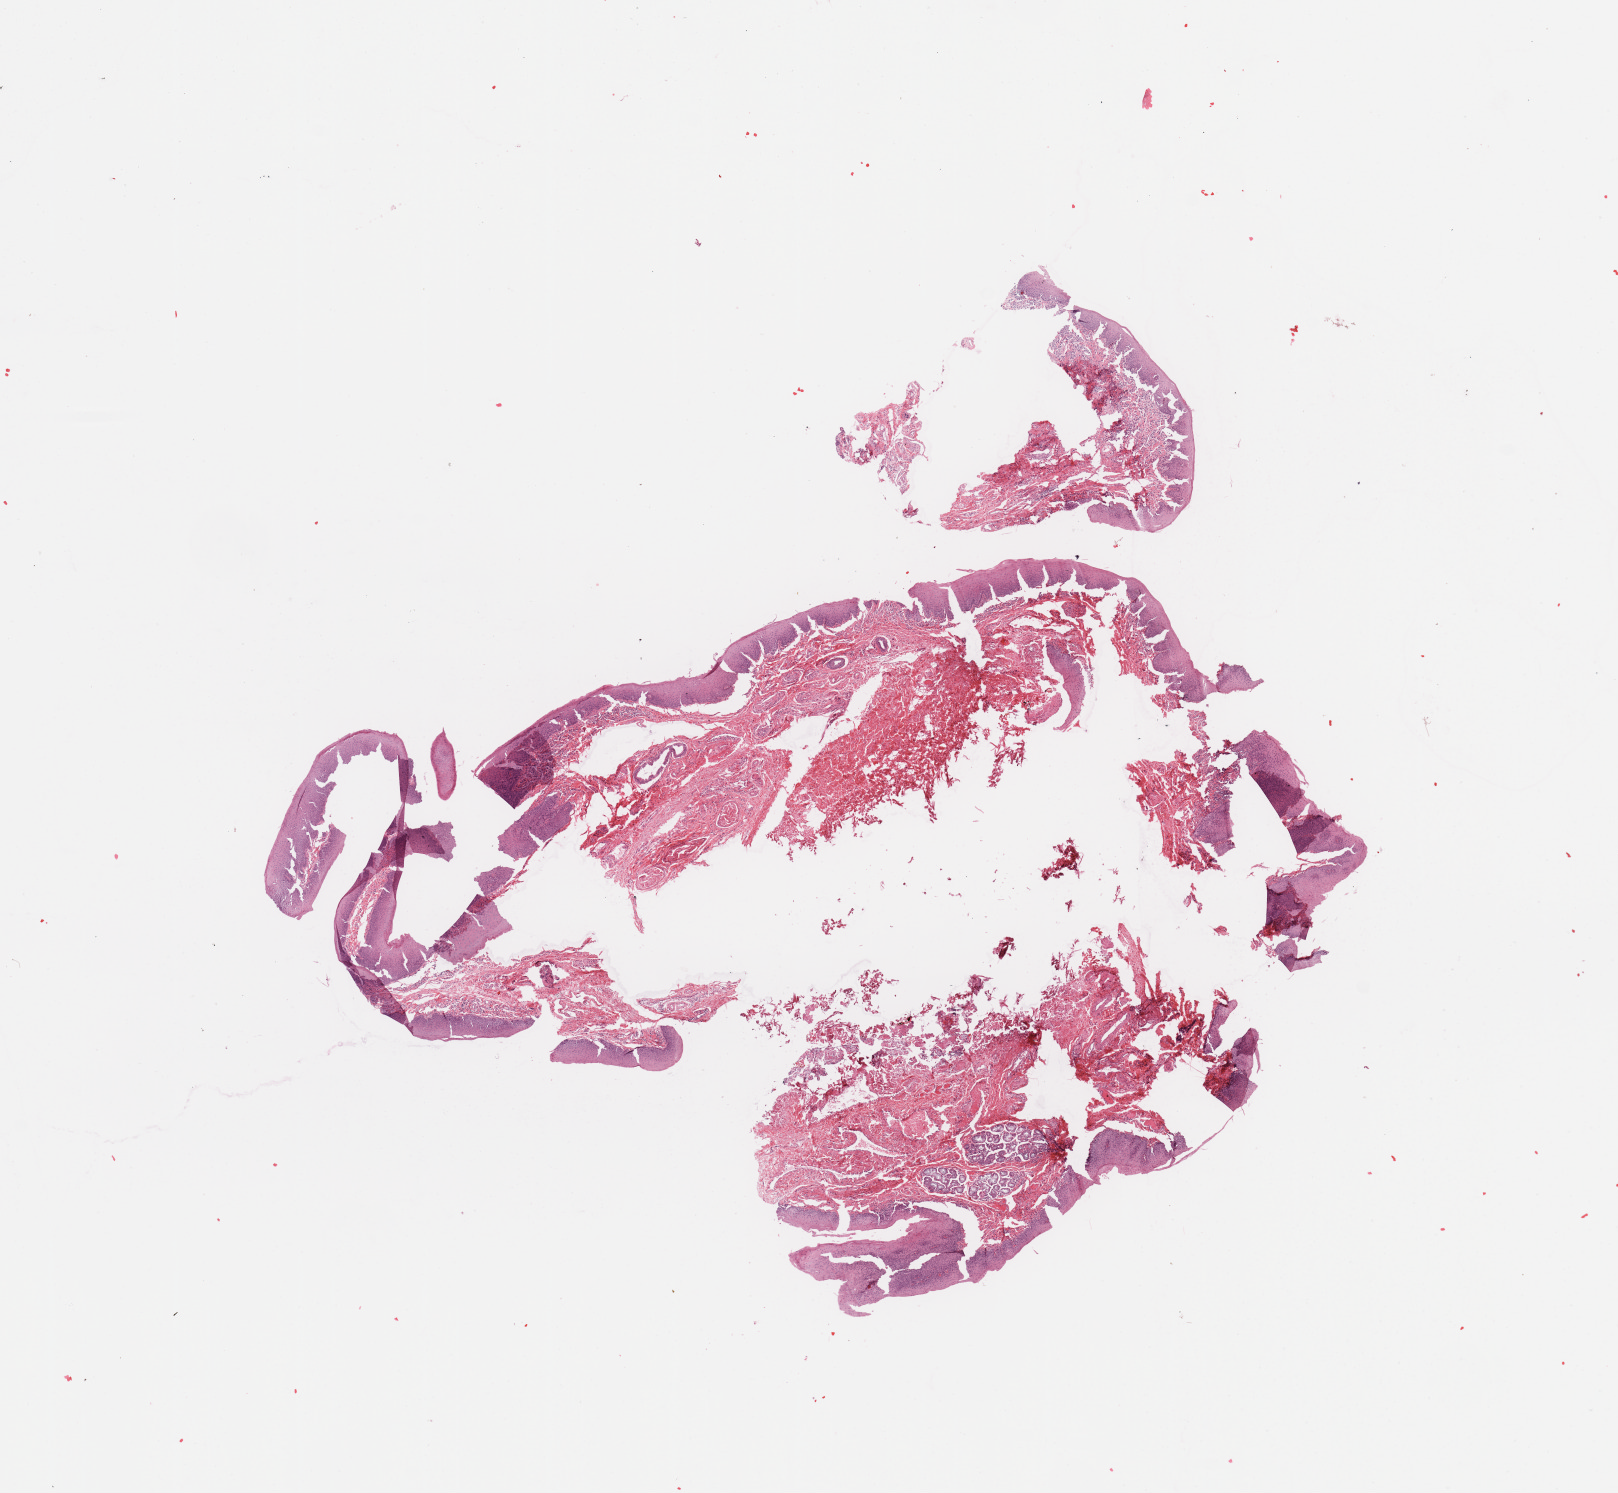
Whole-slide histology image, H&E, shown as a low-resolution overview of the whole scanned area (about 12.8 x 11.8 mm, acquisition: 20x scan), normal (non-tumour) tissue sample, sampled site: larynx. Male, 55 y/o.
This section: normal (non-tumour) tissue from the same patient. Patient diagnosis: Squamous cell carcinoma, NOS (larynx, NOS).